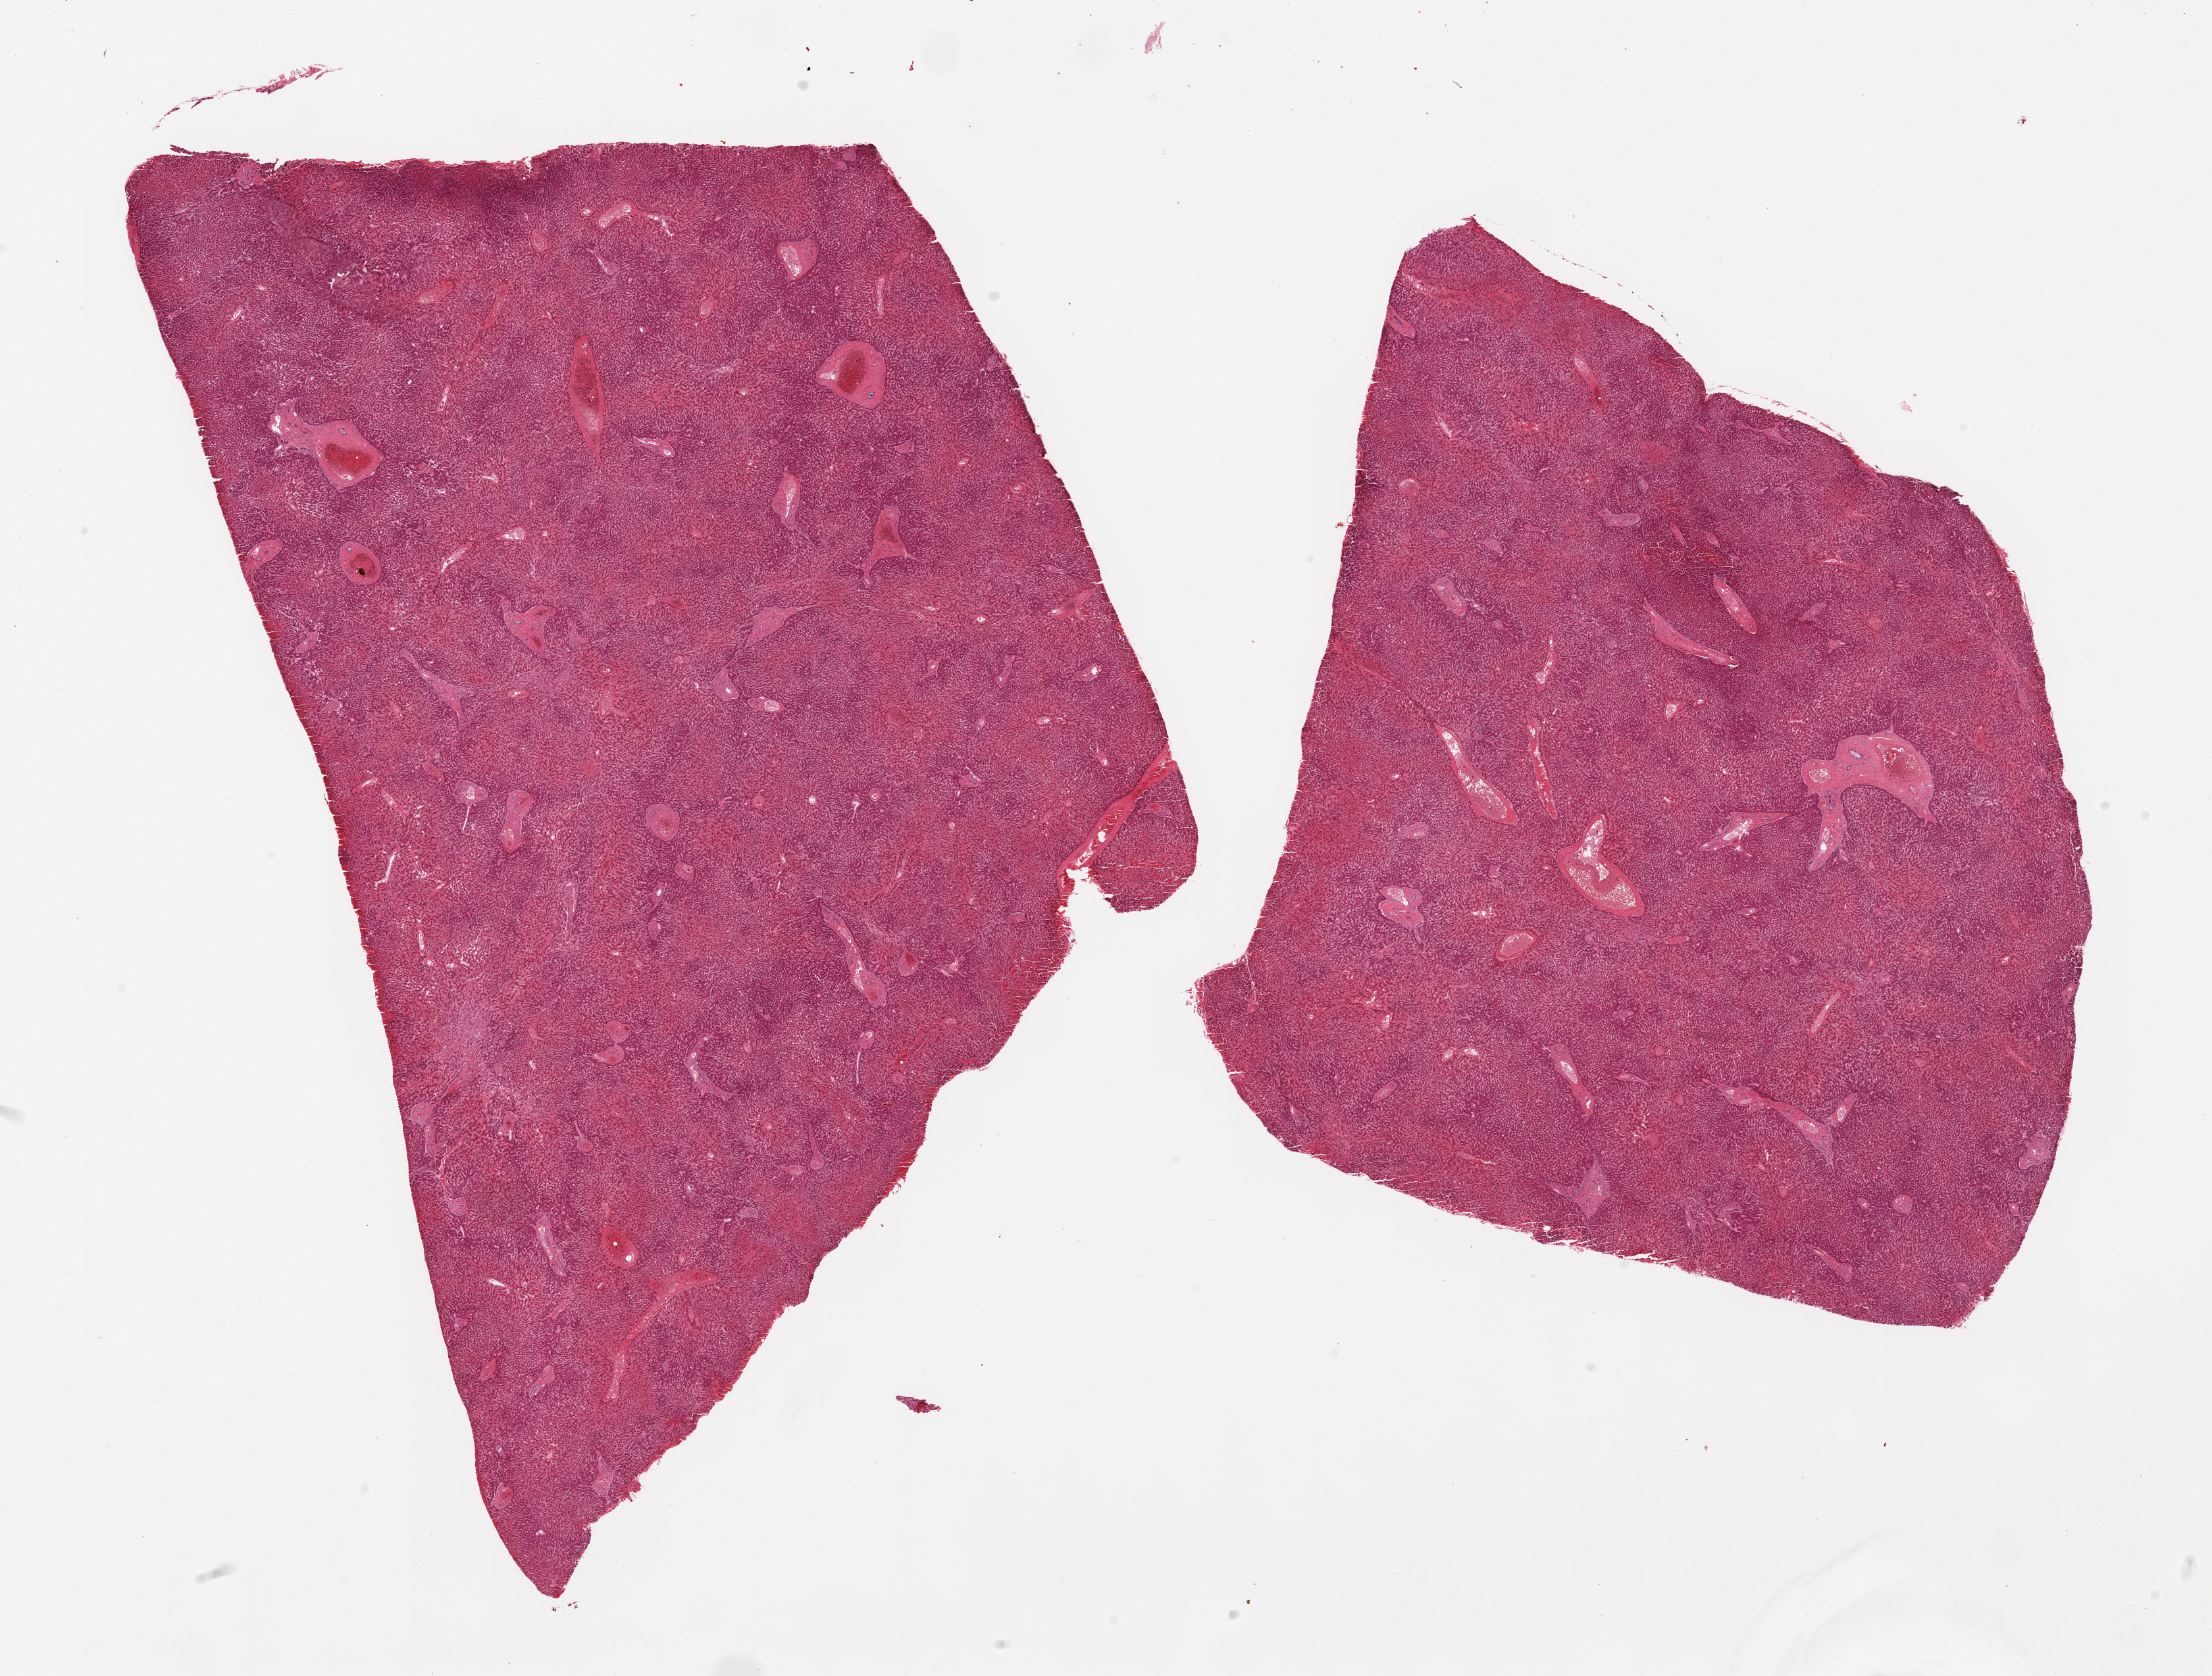
Digitized haematoxylin and eosin-stained section — shown as a low-resolution overview of the whole scanned area (about 26.6 x 20.1 mm, from a 20x scan), PAXgene-fixed, paraffin-embedded tissue, section of liver (target tissue), tissue donor sample. Male donor.
Review note (as recorded): 2 pieces; moderate central congestion with cord cell atrophy; no fat, no fobrosis.